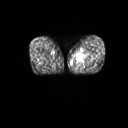
FDG PET of an extremity soft-tissue mass (from a PET/CT study), one axial slice. Position 12 of 267 along the scan axis. 128 × 128 image matrix, field of view 600 × 600 mm. Male patient, age 59 years. From the clinical record (not read from this slice): histological type: pleiomorphic liposarcoma; grade: high; site of the primary tumour: left thigh.
Outlined on this slice (expert contour drawn on MRI and transferred to this co-registered scan by the dataset authors):
- gross tumour volume including surrounding oedema: bounding box (x1, y1, x2, y2) in pixels: (77, 52, 89, 67)